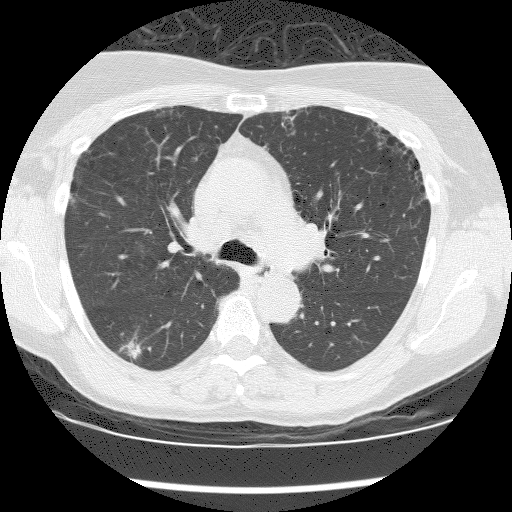
Chest CT (low-dose screening protocol), one axial image. Baseline annual screen. Lung window (W 1500 / L -600 HU). 2.5 mm slice thickness. 120 kVp. 512 × 512 image matrix, field of view 320 × 320 mm. Female, age 59 years at enrolment.
Expert reader's lesion annotation, bounding box <111,338,151,369> (left, top, right, bottom; pixels). The screening reader recorded 6 non-calcified nodules or masses ≥4 mm on this exam (right upper lobe, right upper lobe, right lower lobe, right lower lobe, right upper lobe, right upper lobe); which of them this box marks is not recorded. Later outcome: lung cancer diagnosed 242 days after this screen — adenocarcinoma, NOS, right lower lobe, moderately differentiated (G2), stage IIIA (AJCC 6th edition), 12 mm at pathology.